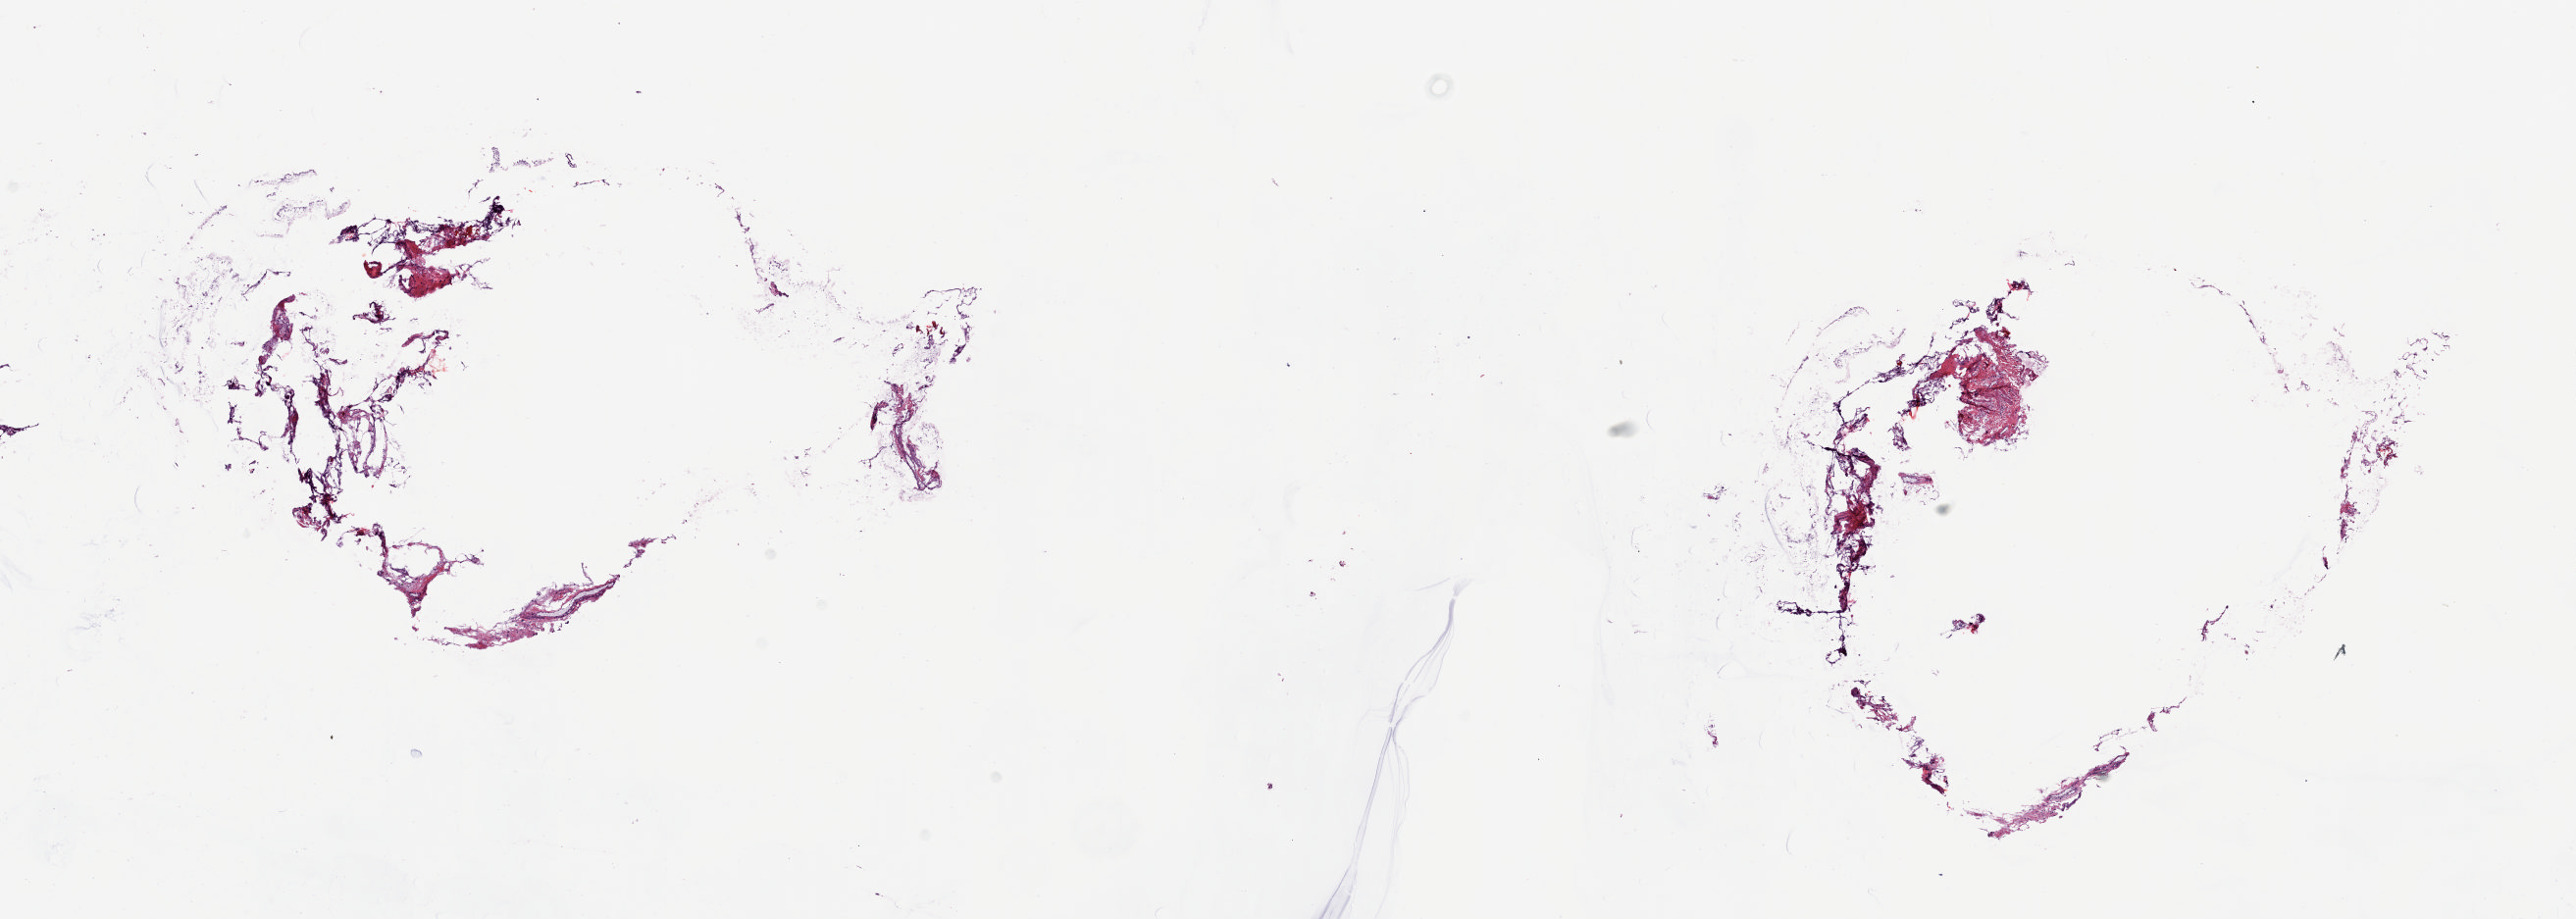
Digitized H&E-stained tissue section (whole slide) — a low-resolution overview of the entire scanned area, about 20.8 x 7.4 mm, frozen section from the top of the tissue portion, sample: solid tissue normal (non-tumour tissue), thymus. Patient: female, age at initial diagnosis 40 years. Pathologist review of this section (percent, as recorded): tumour cells 0%, tumour nuclei 0%, normal cells 100%, stromal cells 0%, necrosis 0%. Inflammatory infiltration, as recorded: lymphocyte infiltration 0%, monocyte infiltration 0%, neutrophil infiltration 0%.
* this section: solid tissue normal sample (biorepository sample class)
* patient diagnosis: Thymoma, type B3, malignant